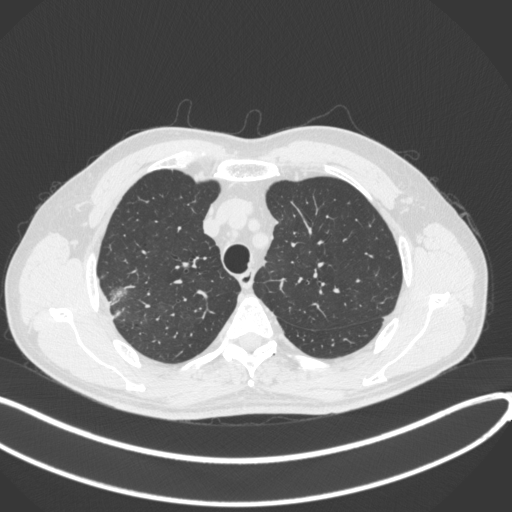
Chest CT, one axial slice. Position 333 of 381 along the scan axis. Lung window (W 1500 / L -600 HU). 1 mm slice thickness. 512 × 512 image matrix. Patient: male, 62 years. Case-level facts recorded for this patient, not image findings: clinical TNM (as recorded): T1c N0 M0; histopathological grade: G2-3.
Structures marked on this image (bounding box drawn by a radiologist):
- lung tumour (recorded histology: adenocarcinoma): bounding box [x1, y1, x2, y2] px = [105, 283, 131, 319]